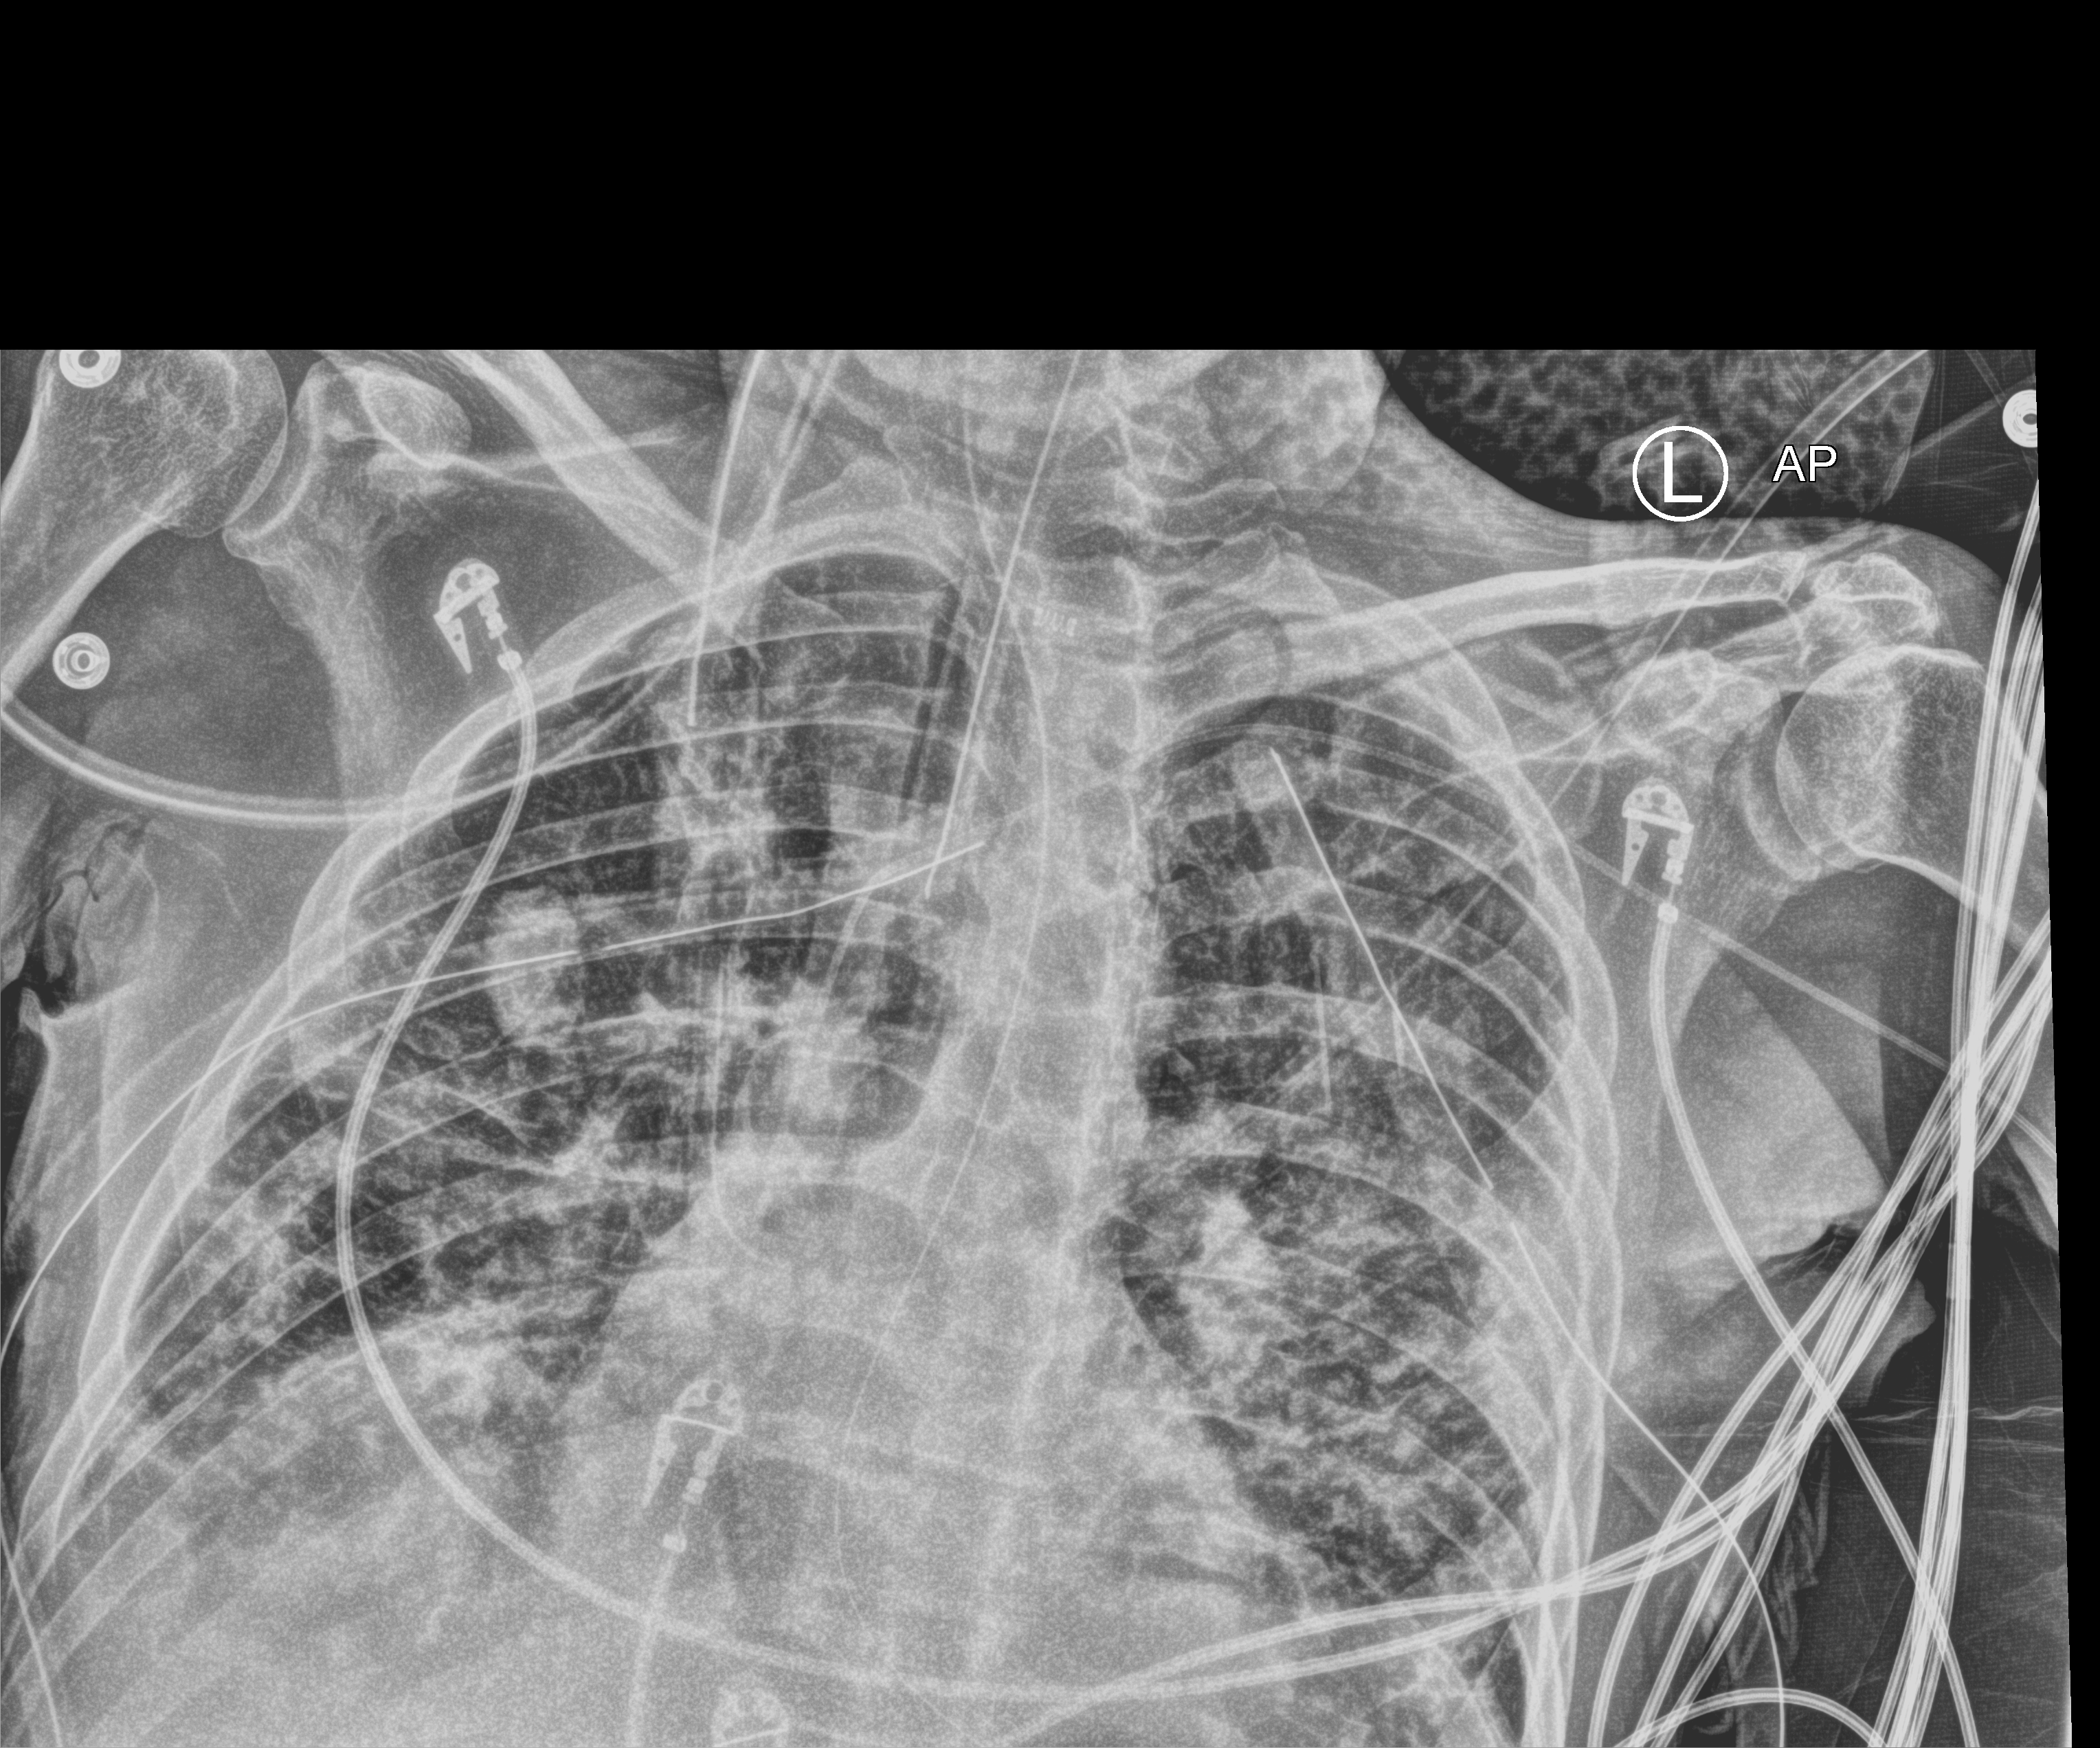
Bedside chest radiograph (computed radiography). Patient hospitalised with COVID-19; male, aged 18–59 years.
Admission-level facts for this patient (not findings on this image; timing relative to this image not recorded):
- hypertension (admission record): yes
- admitted to intensive care during this hospital stay: yes
- mechanically ventilated during this hospital stay: yes